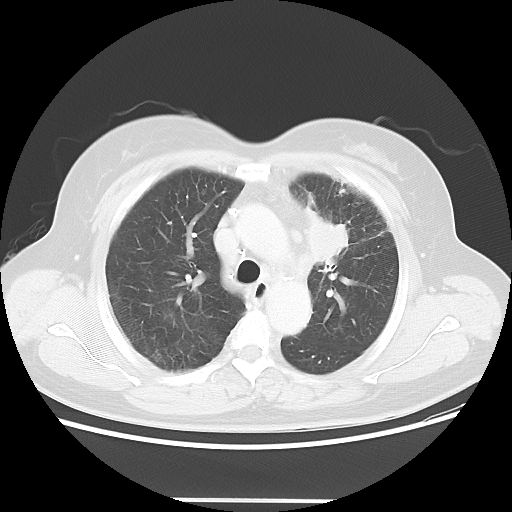
Chest CT, one axial slice. Position 39 of 52 along the scan axis. 120 kVp. Lung window (W 1500 / L -600 HU). 5 mm slice thickness. 512 × 512 image matrix, field of view 382 × 382 mm. Female patient, age 52 years. Case-level facts recorded for this patient, not image findings: clinical TNM (as recorded): T2 N3 M0.
Outlined on this slice (bounding box drawn by a radiologist):
- lung tumour (recorded histology: adenocarcinoma): bounding box <298,199,351,266> (left, top, right, bottom; pixels)